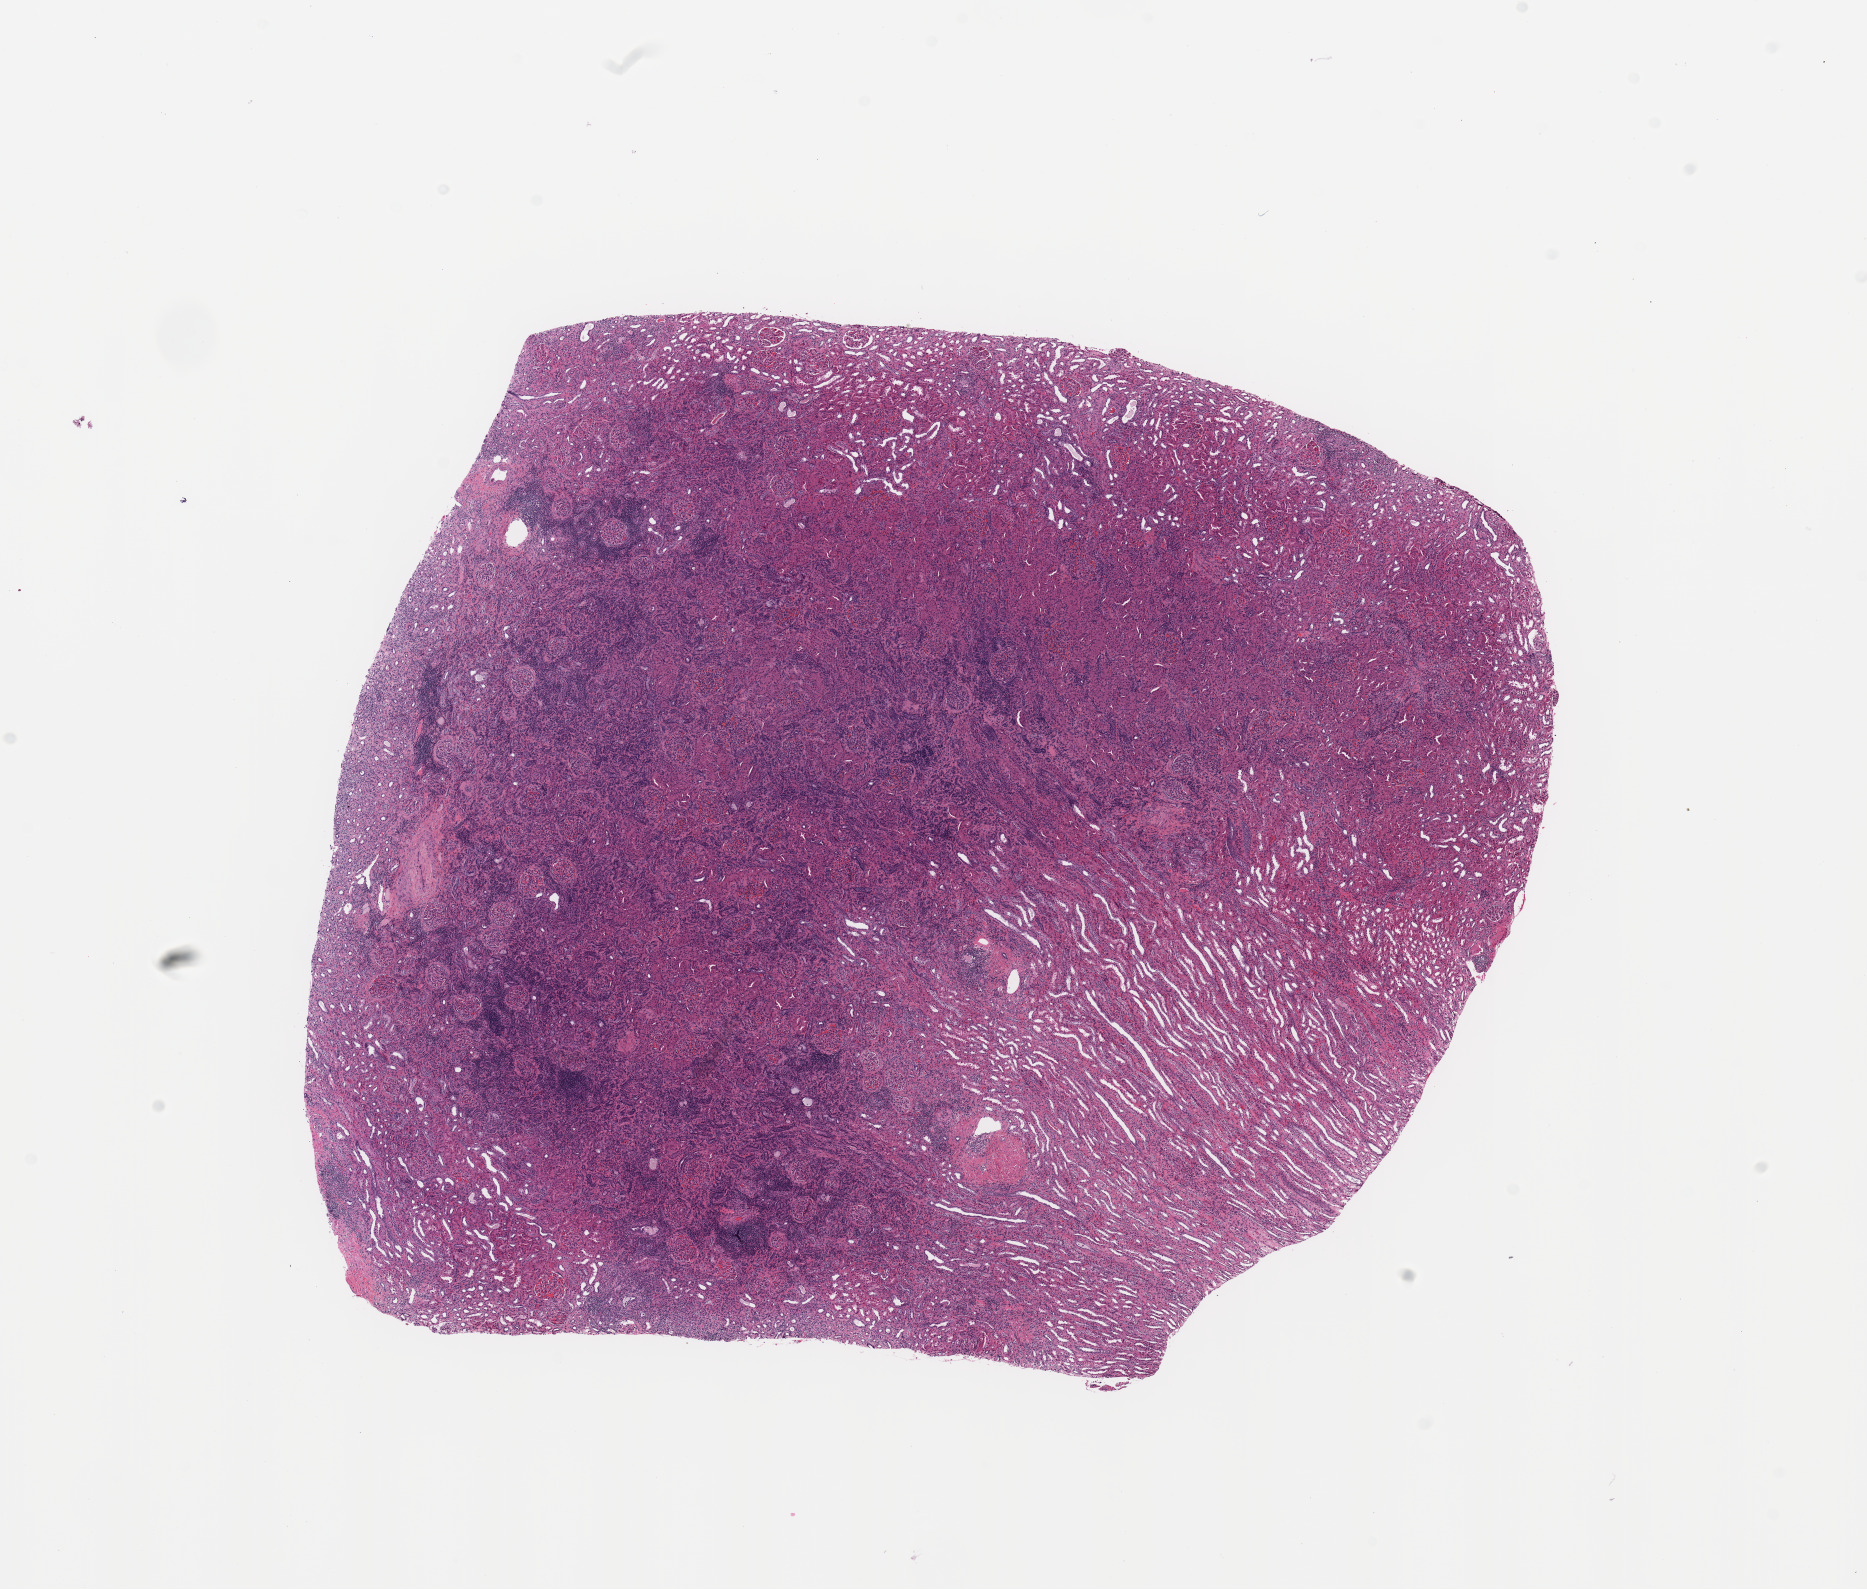
Whole-slide histology image, H&E, a low-resolution overview of the entire scanned area, about 14.8 x 12.6 mm, normal (non-tumour) tissue sample, kidney. Patient: male, age 40 years.
This section: normal (non-tumour) tissue from the same patient. Patient diagnosis: Renal cell carcinoma, NOS.